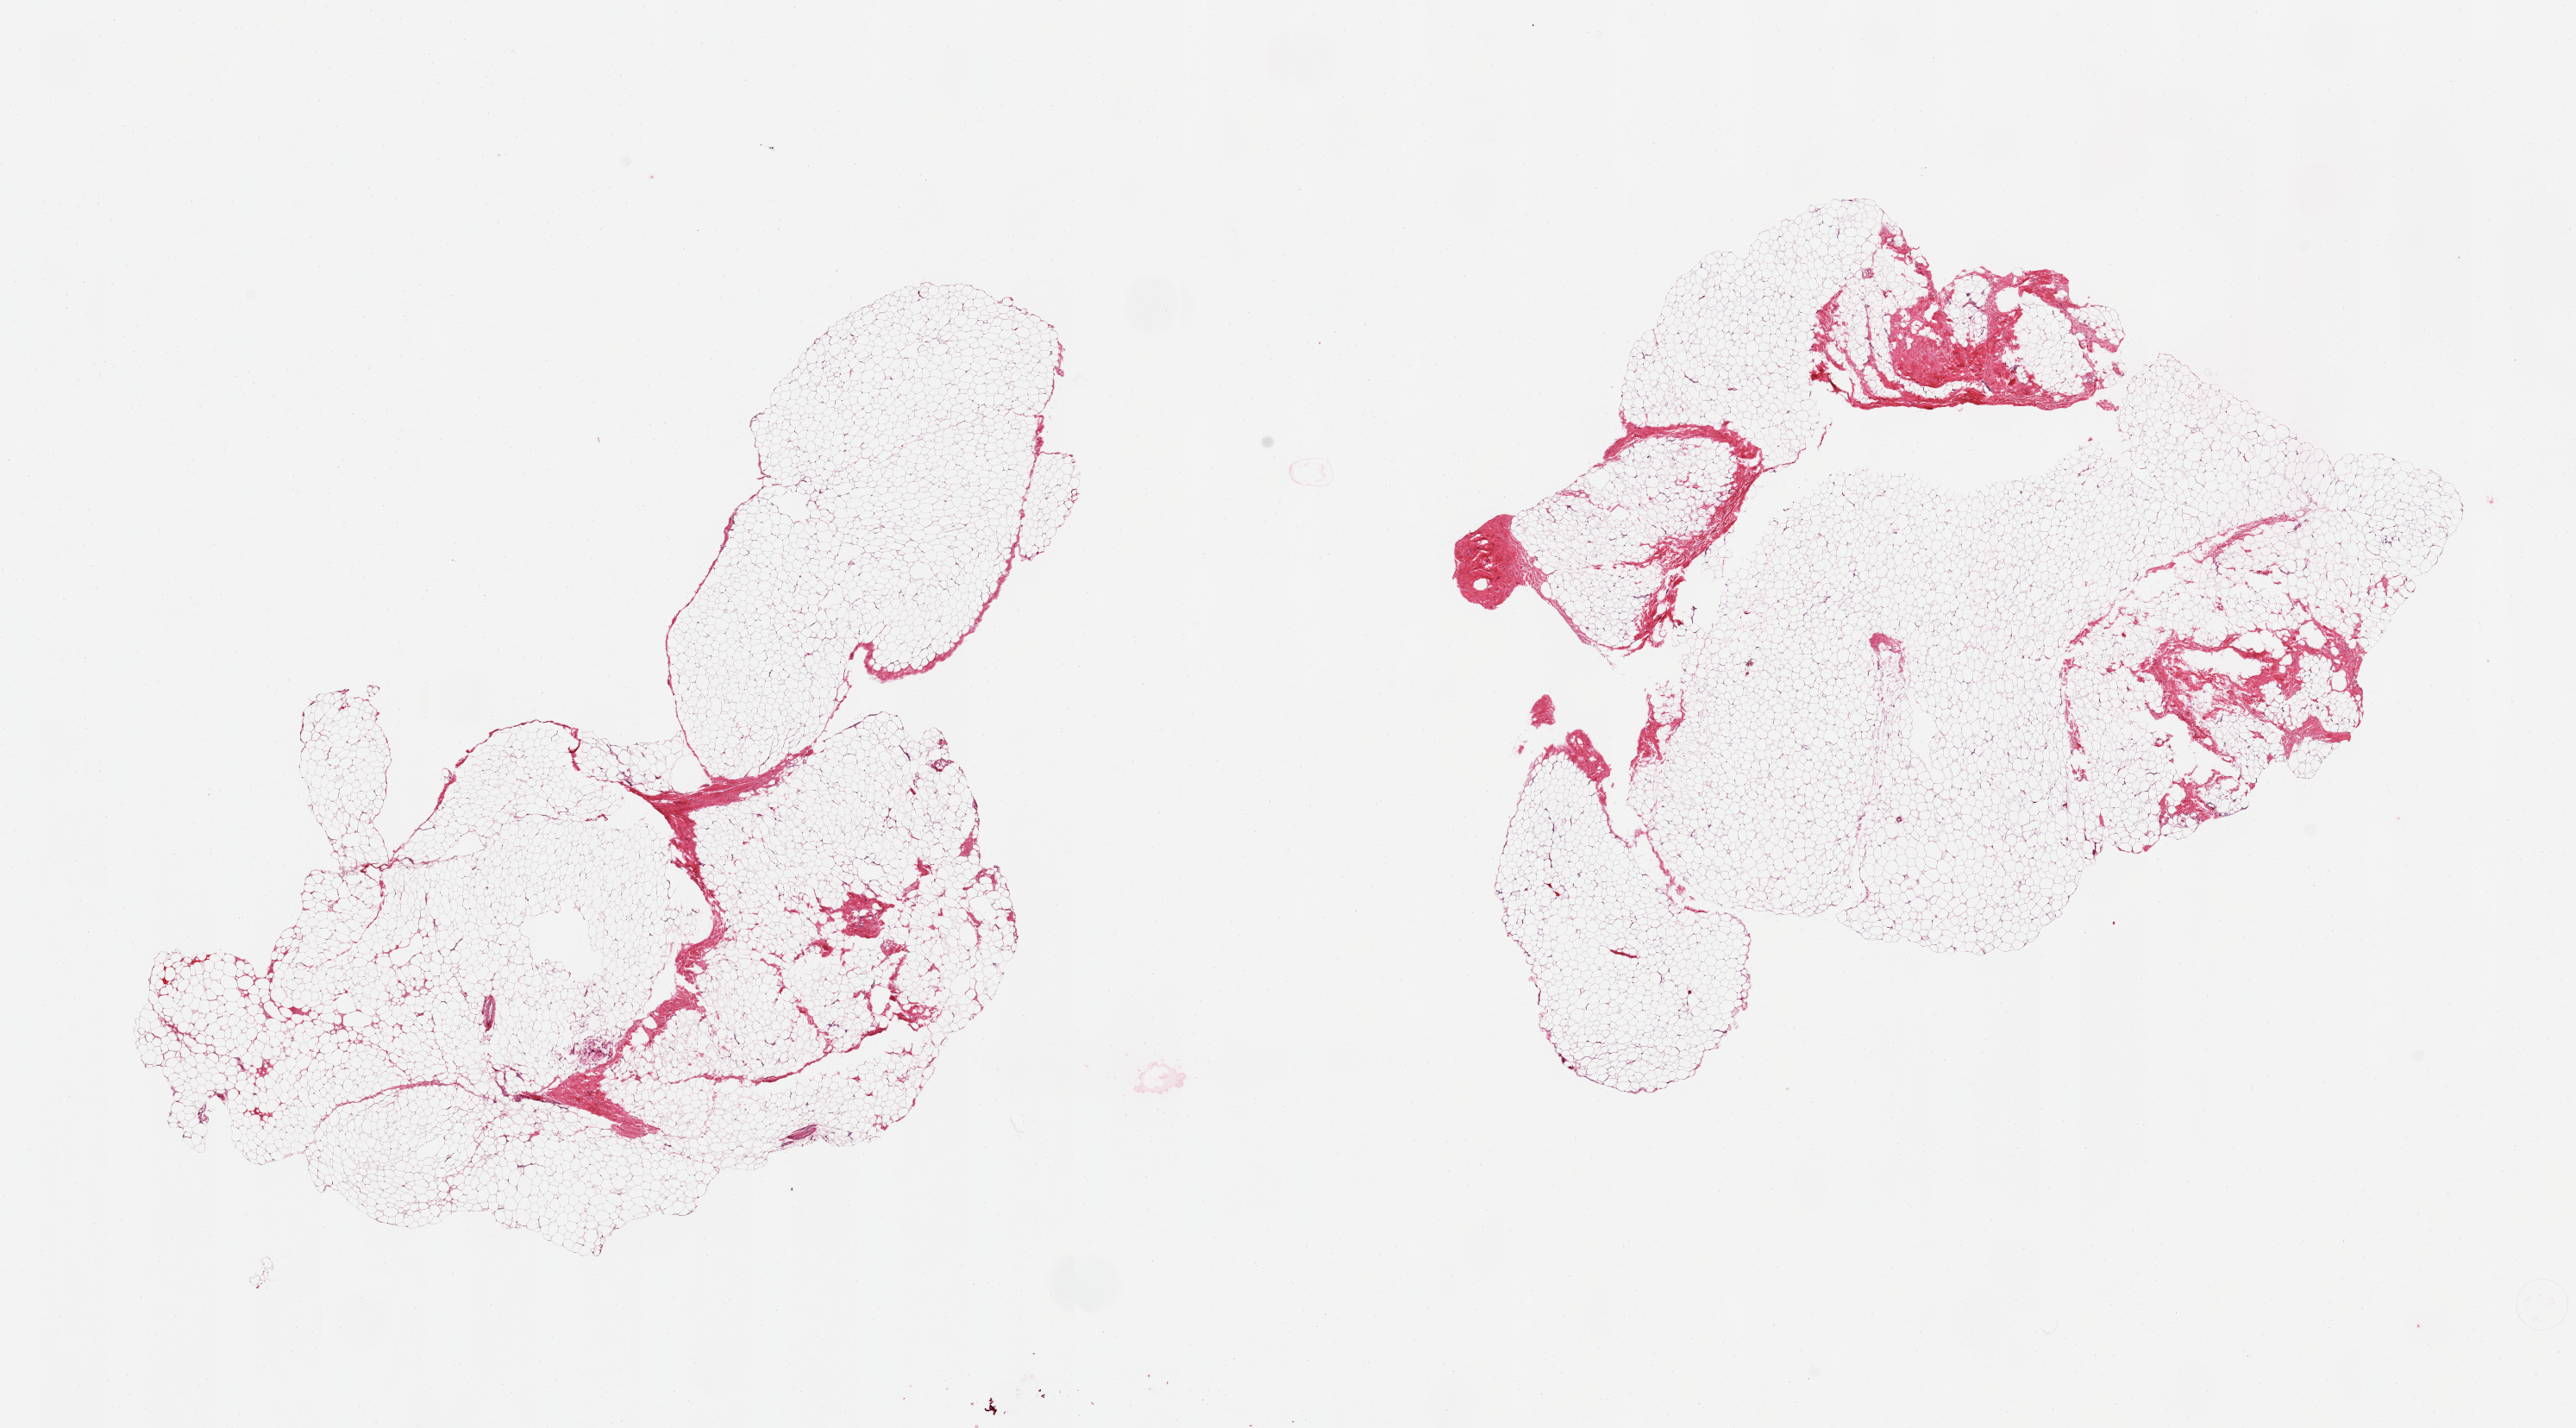
Digitized hematoxylin and eosin (H&E)-stained section, whole scanned area (about 23.6 x 13.1 mm) shown as a low-resolution overview, PAXgene-fixed paraffin-embedded (PFPE) section, target tissue: breast, tissue donor sample.
Pathologist's review note for this sample: 2 pieces, fibroadipose elements only.